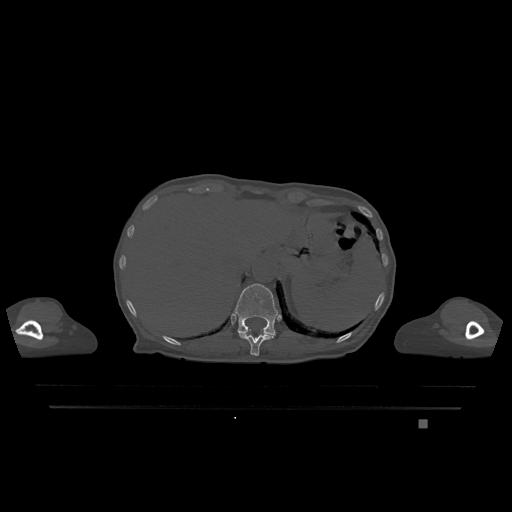
CT including the spine, one axial slice. Position 556 of 1317 along the scan axis. Bone window (W 1800 / L 400 HU). 0.5 mm slice thickness. 512 × 512 image matrix, field of view 500 × 500 mm. Patient: female, 74 years. From the clinical record (not read from this slice): primary cancer: lung.
Outlined on this slice (semi-automatic segmentation, software-assisted and operator-edited):
- T11 vertebra: bounding box [x1, y1, x2, y2] px = [239, 333, 275, 356]
- T12 vertebra: [234, 284, 278, 336]